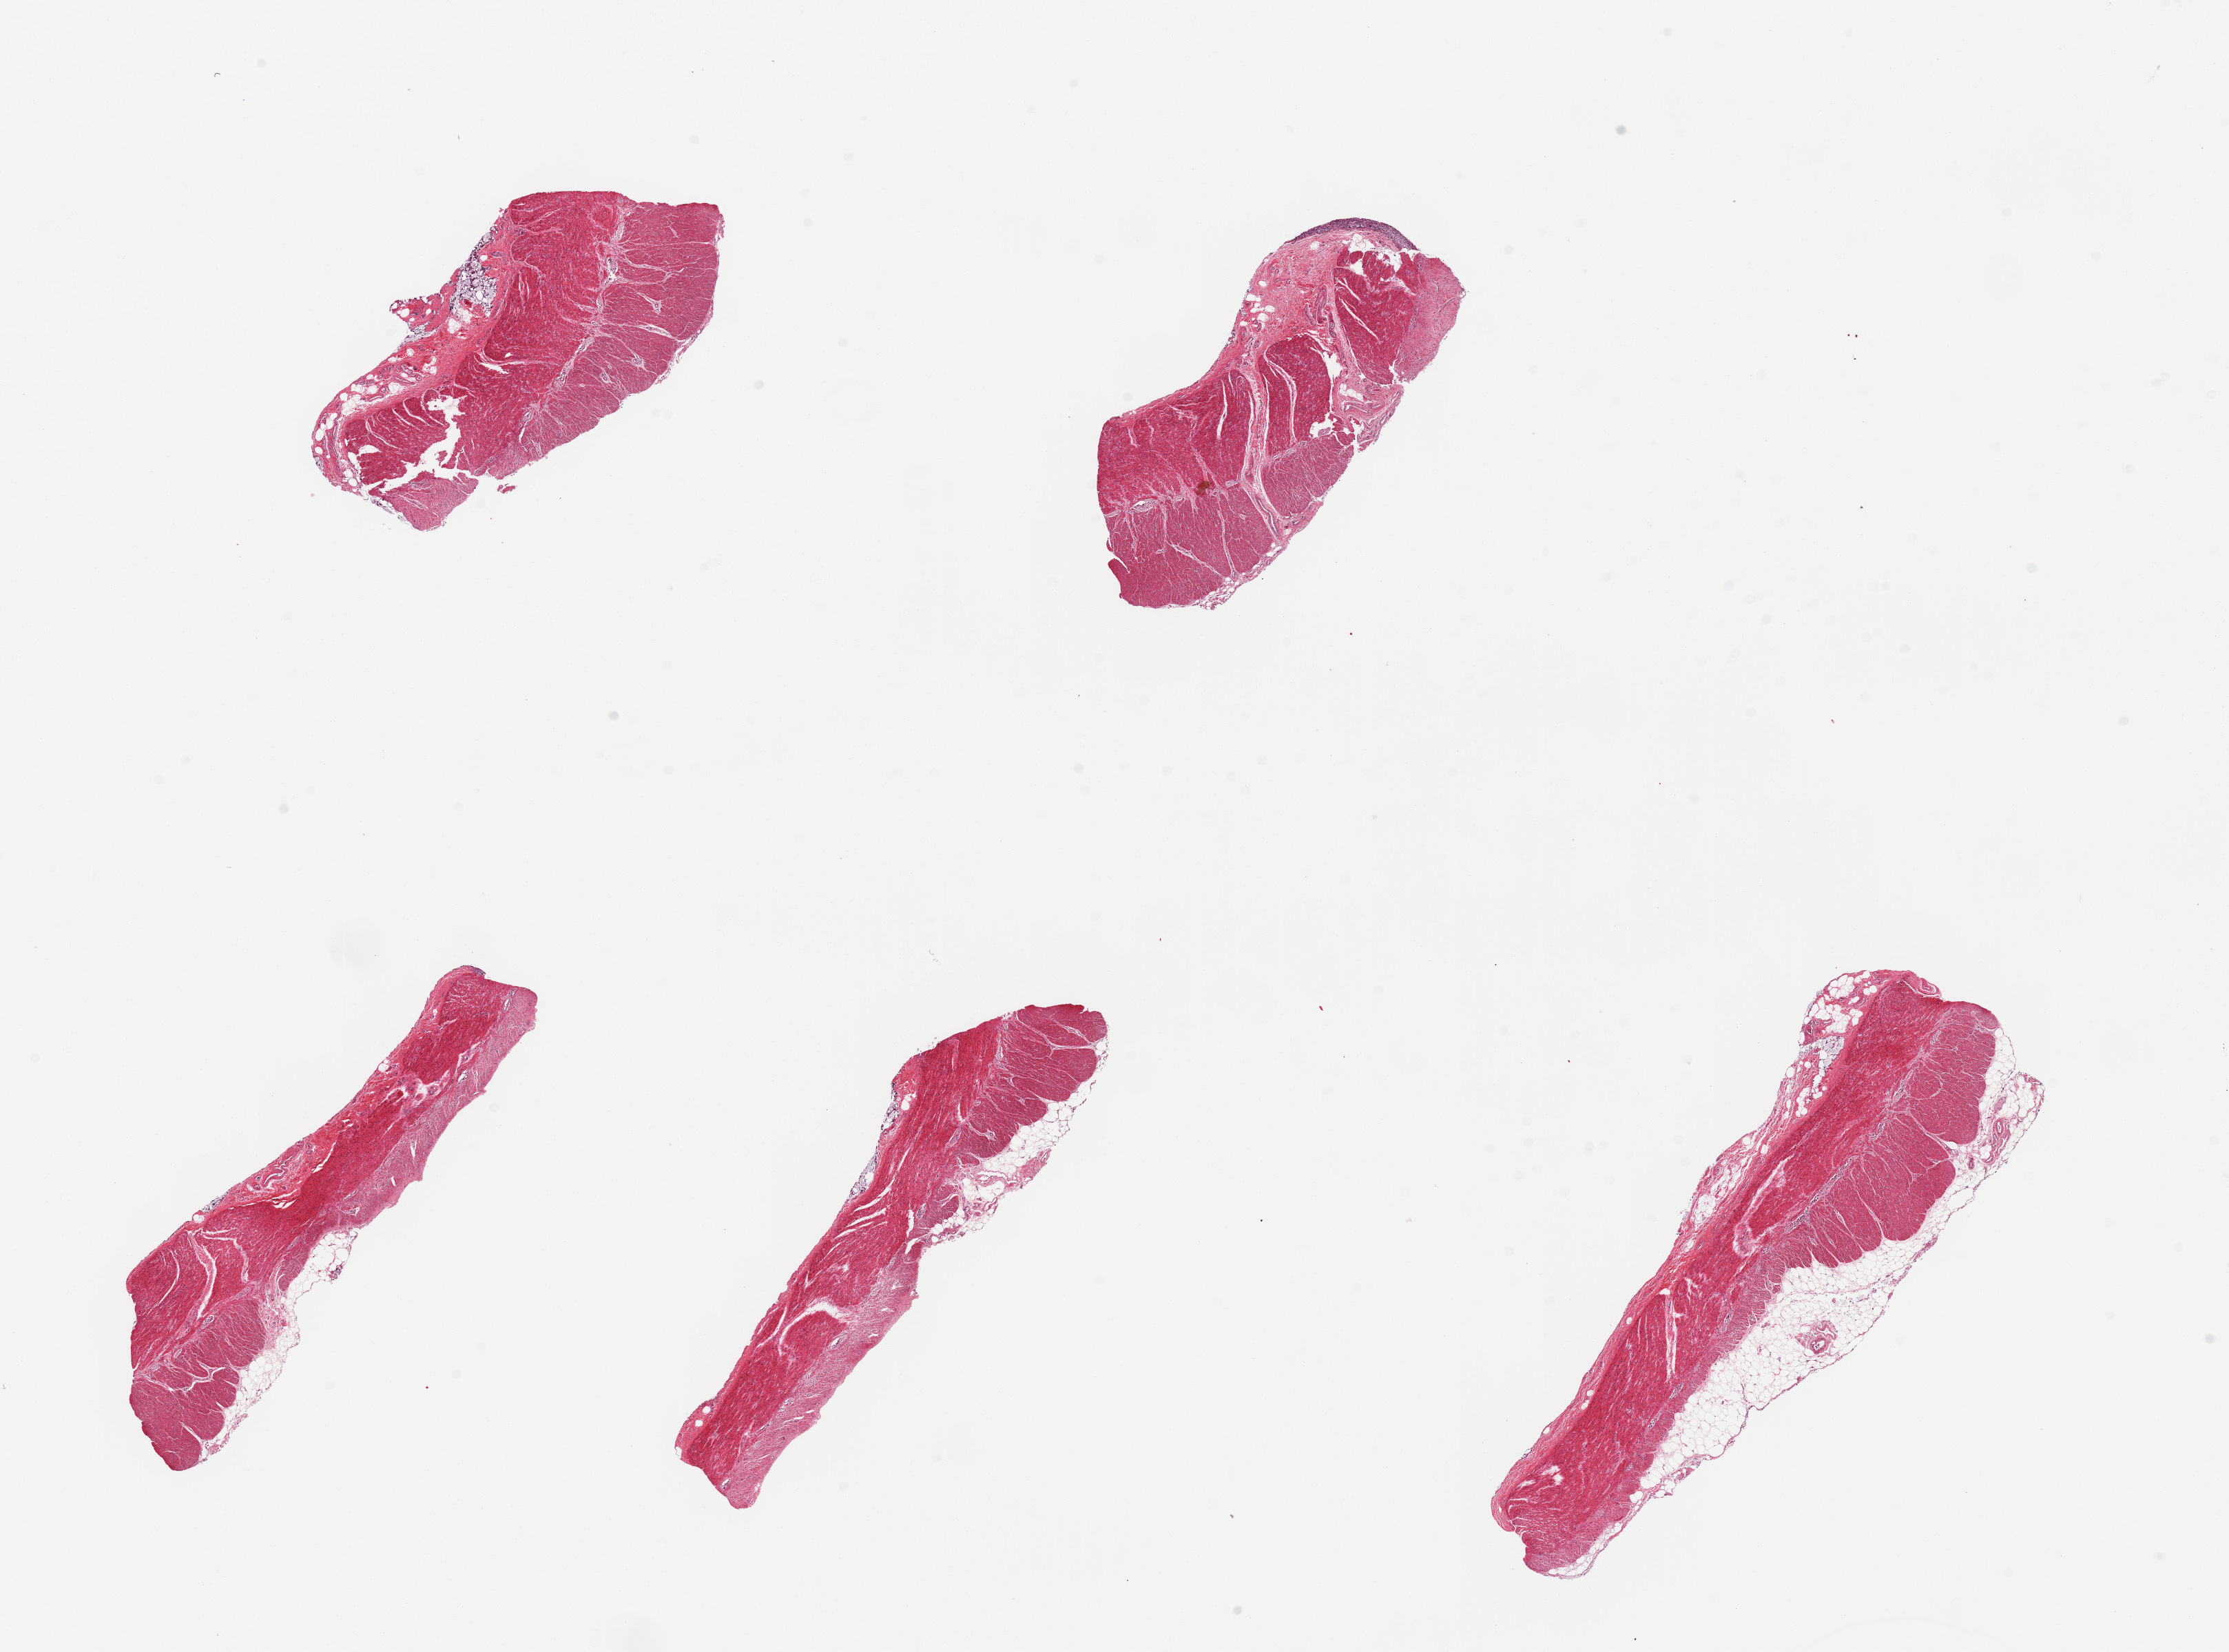
H&E whole-slide image — low-resolution overview of the scanned area, about 25.6 x 19.0 mm (slide scanned at 20x); PAXgene-fixed, paraffin-embedded tissue; section of sigmoid colon (target tissue); donor tissue sample. Donor: female.
- reviewer comment on this tissue sample: 5 pieces; predominantly muscularis with scant residual mucosa and fat